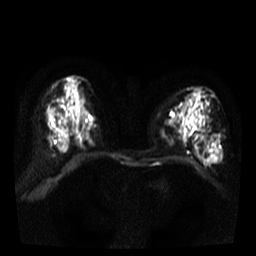
Breast MRI, one axial slice. Slice 22 of 38 in the series (ordered by position). Diffusion-weighted series; image 2 of 4 stored at this slice position (different b-values; order by instance number). 3 T. 256 × 256 image matrix. Female patient.
Annotated regions visible in this slice (outlined manually by an expert reader):
- tumour on diffusion-weighted imaging: bounding box [x1, y1, x2, y2] px = [214, 149, 219, 155]